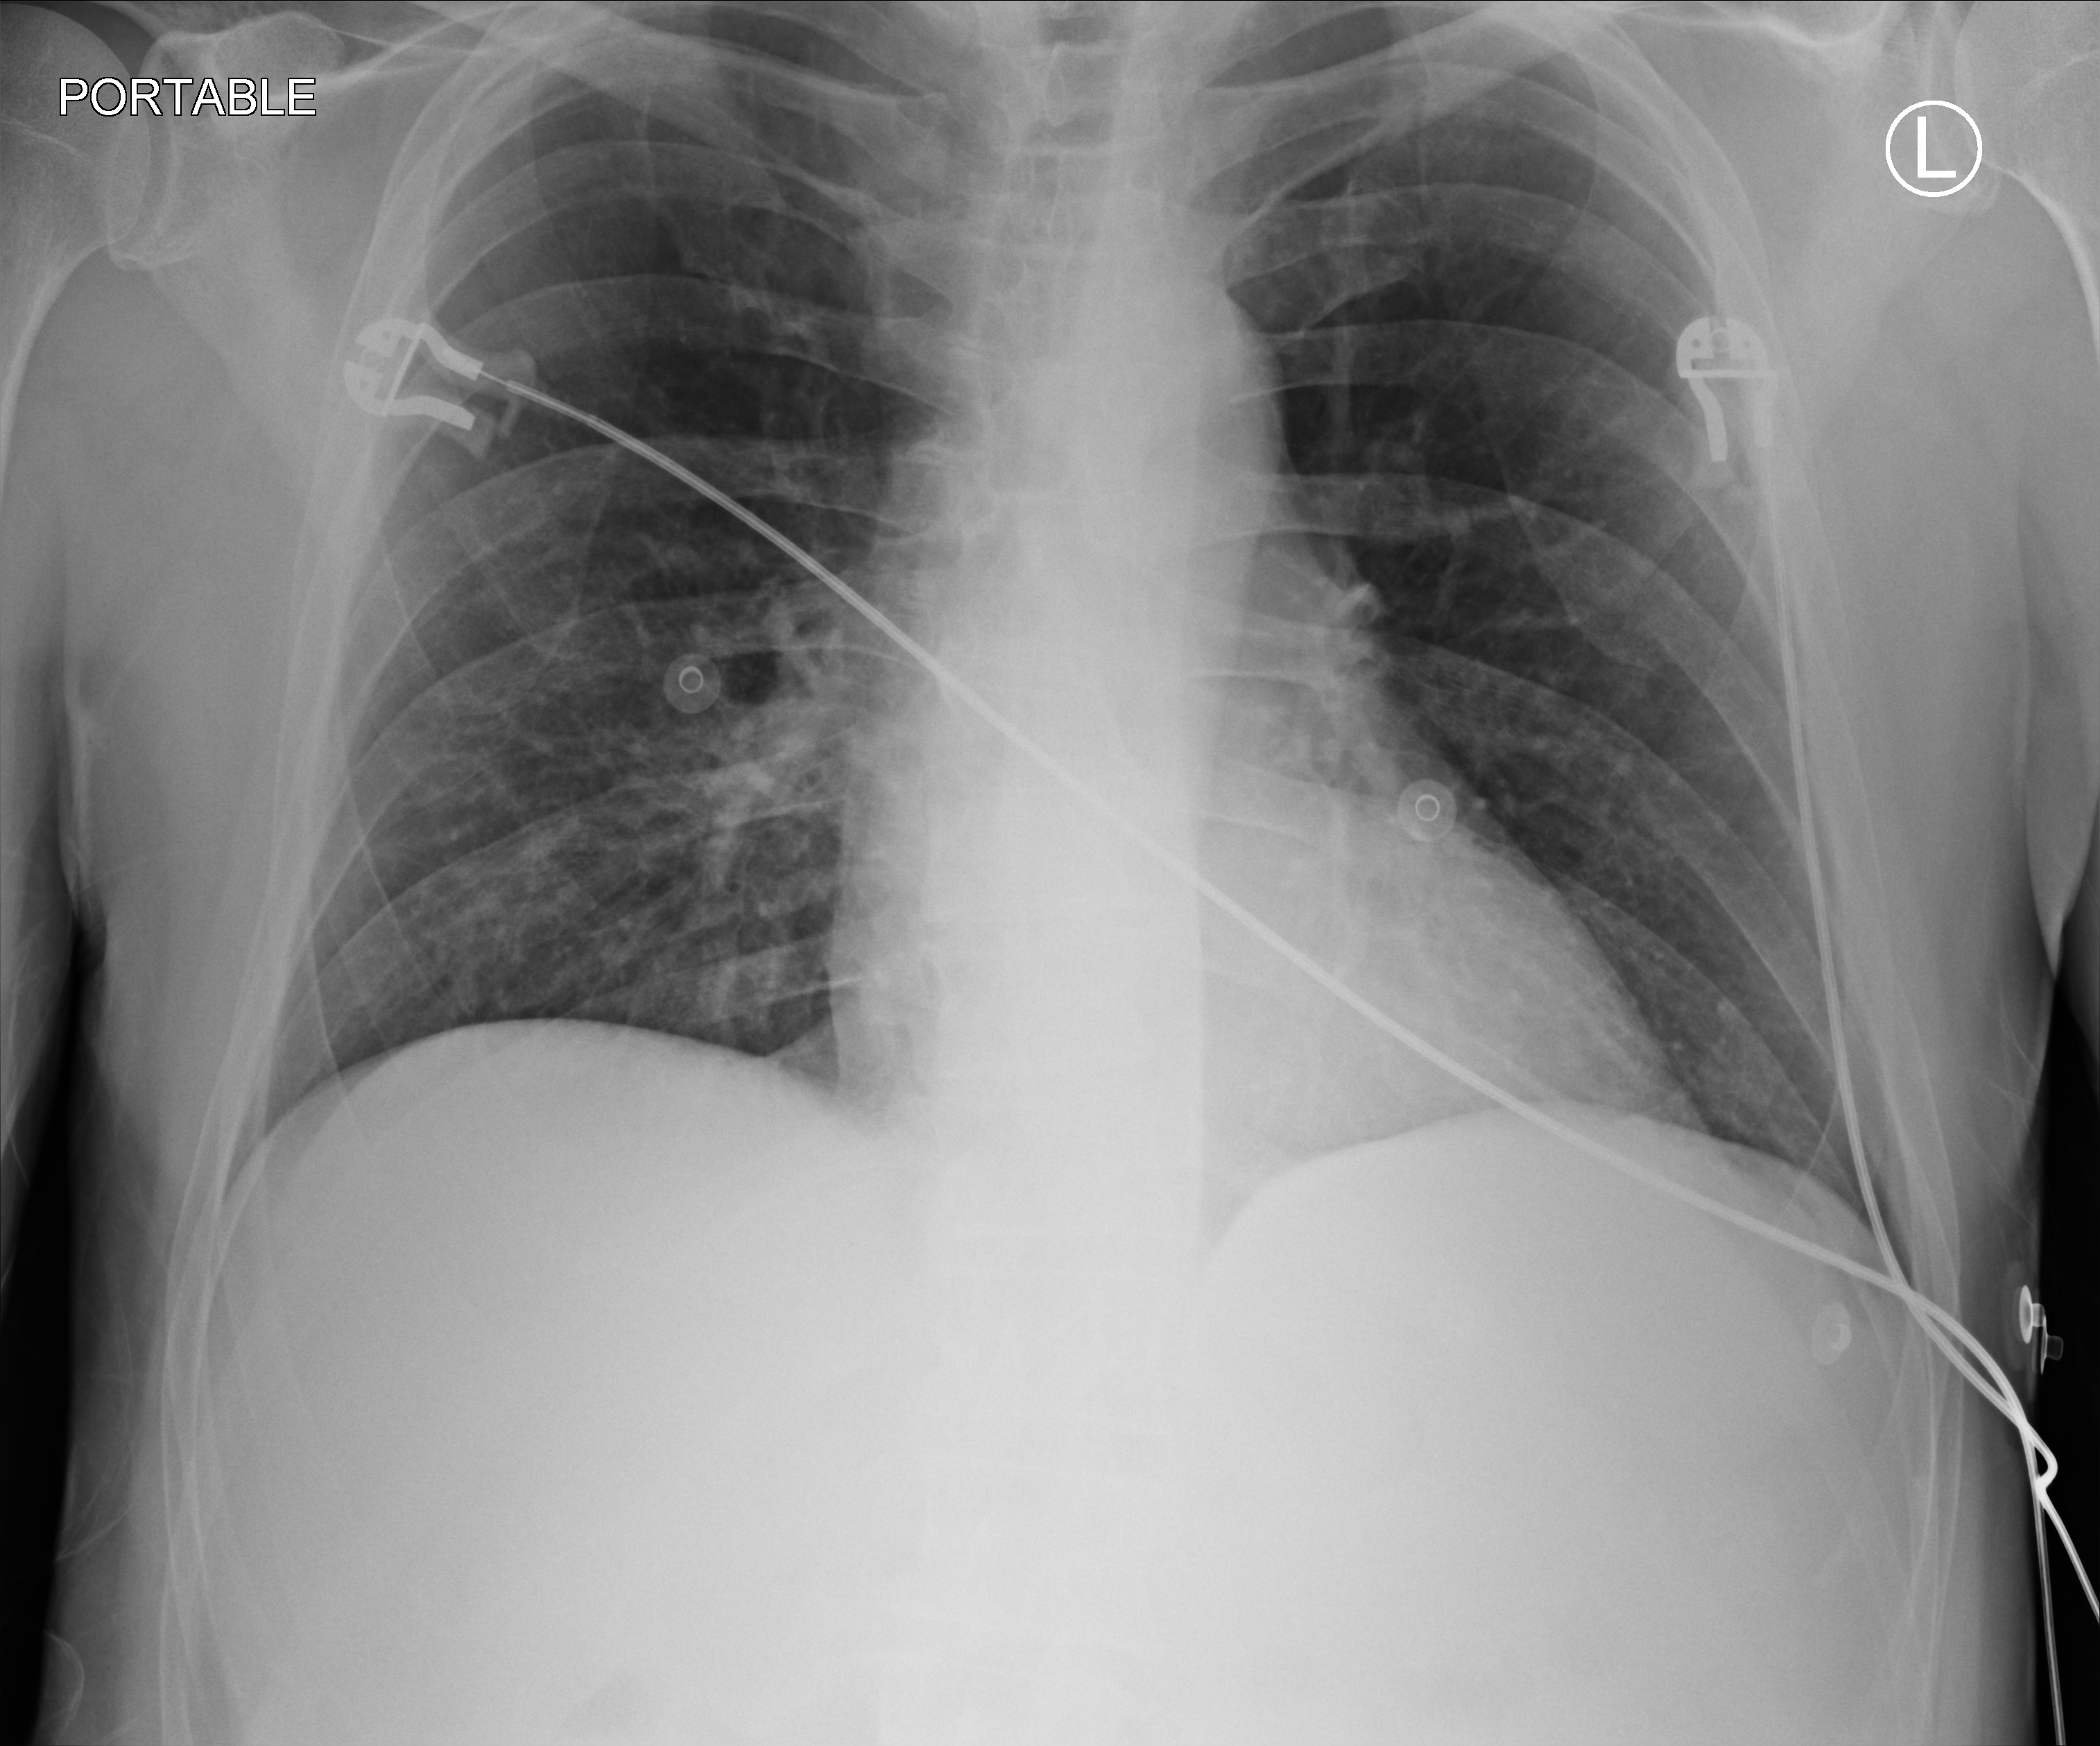
Bedside chest radiograph (computed radiography), anteroposterior (AP) projection. Male patient hospitalised with COVID-19, age 60–74 years.
Hospital-stay facts (about this admission, not read from this image; timing relative to this image not recorded): admitted to intensive care during this hospital stay: no; mechanically ventilated during this hospital stay: no.